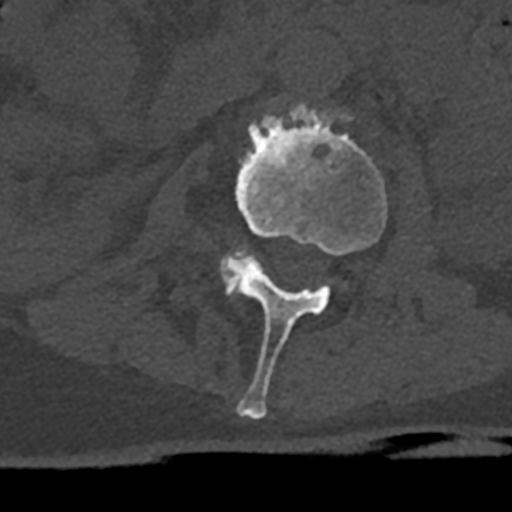
CT including the spine, one axial slice; slice 367 of 797 in the series (ordered by position); reconstruction kernel Br40s/3; 120 kVp; bone window (W 1800 / L 400 HU); 512 × 512 image matrix. Patient: male, 74 years. Case-level facts recorded for this patient, not image findings: primary cancer: renal; vertebrae with lytic lesions (as recorded): T10, L1, L2, L3, L4, L5.
Annotated regions visible in this slice (semi-automatically segmented with operator editing):
- L2 vertebra: bounding box (x1, y1, x2, y2) in pixels: (219, 104, 387, 419)
- L3 vertebra: (222, 250, 255, 296)